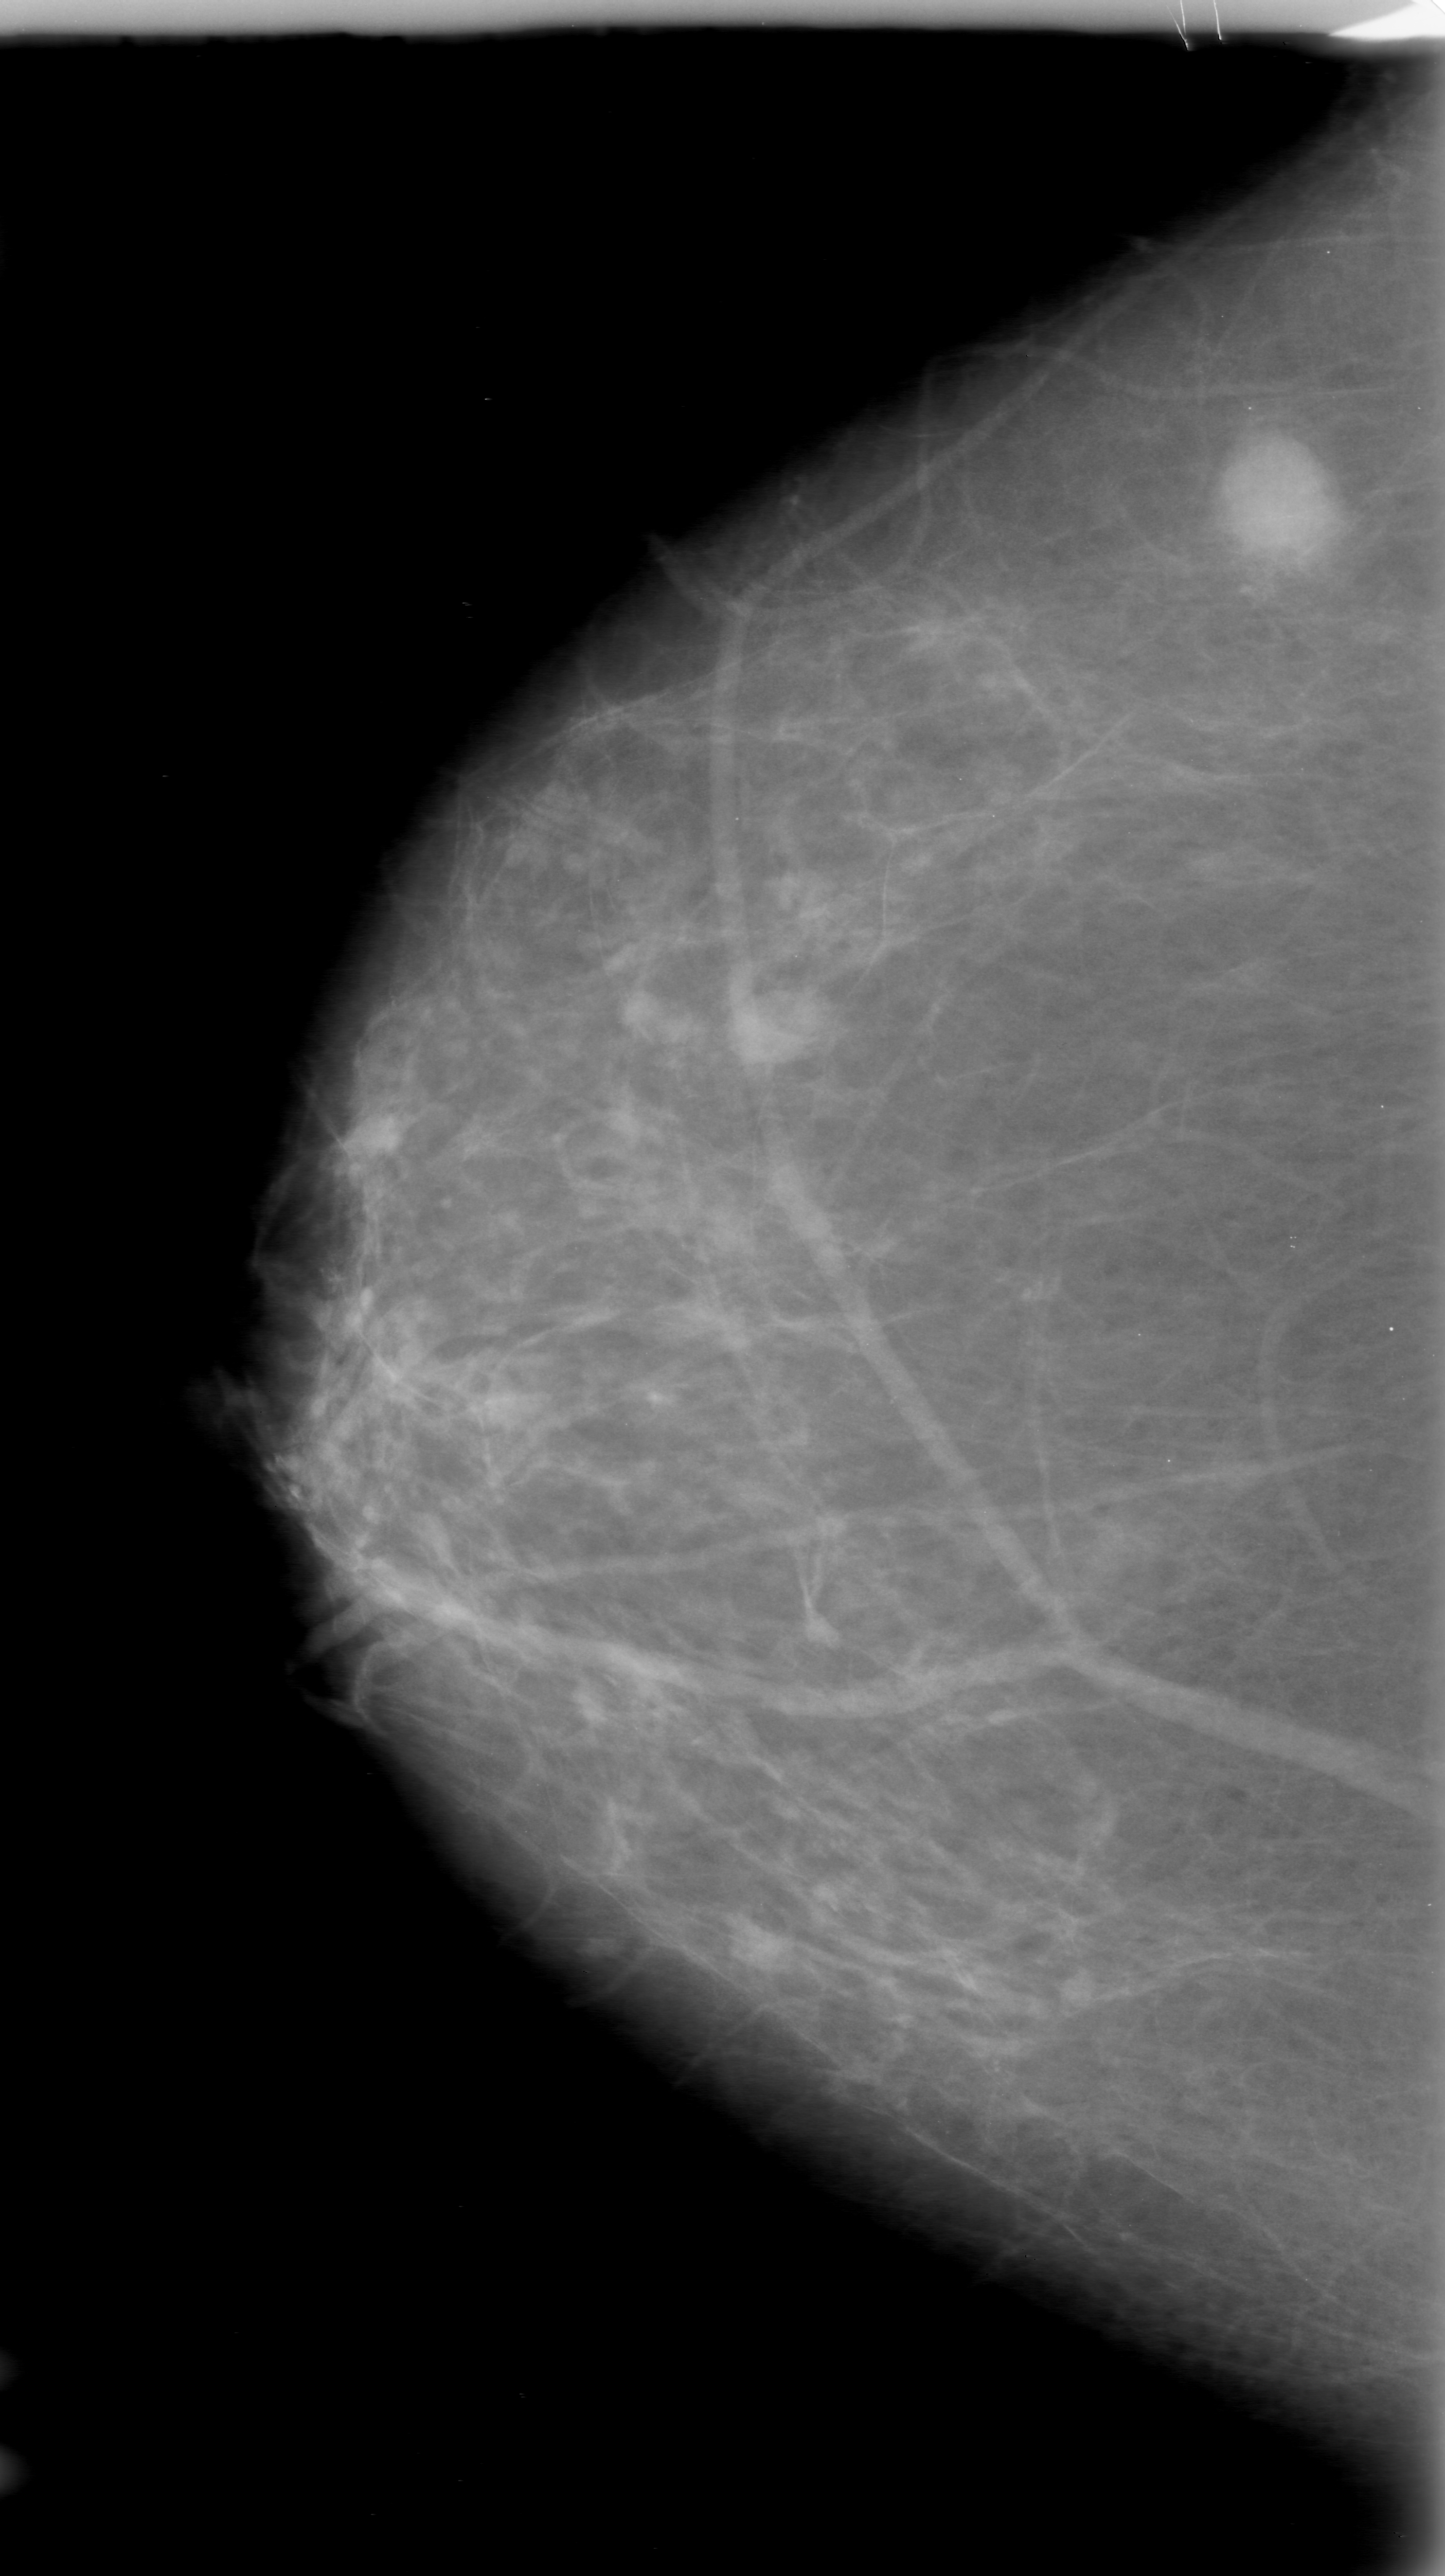
Digitized screen-film mammogram; right breast; craniocaudal (CC) view; BI-RADS breast density category 2 (scale 1–4).
Mass, shape round, margins ill defined; BI-RADS assessment category 5; subtlety rating 5 on a 1 (subtle) to 5 (obvious) scale; pathology result (as recorded, not read from the image): malignant.